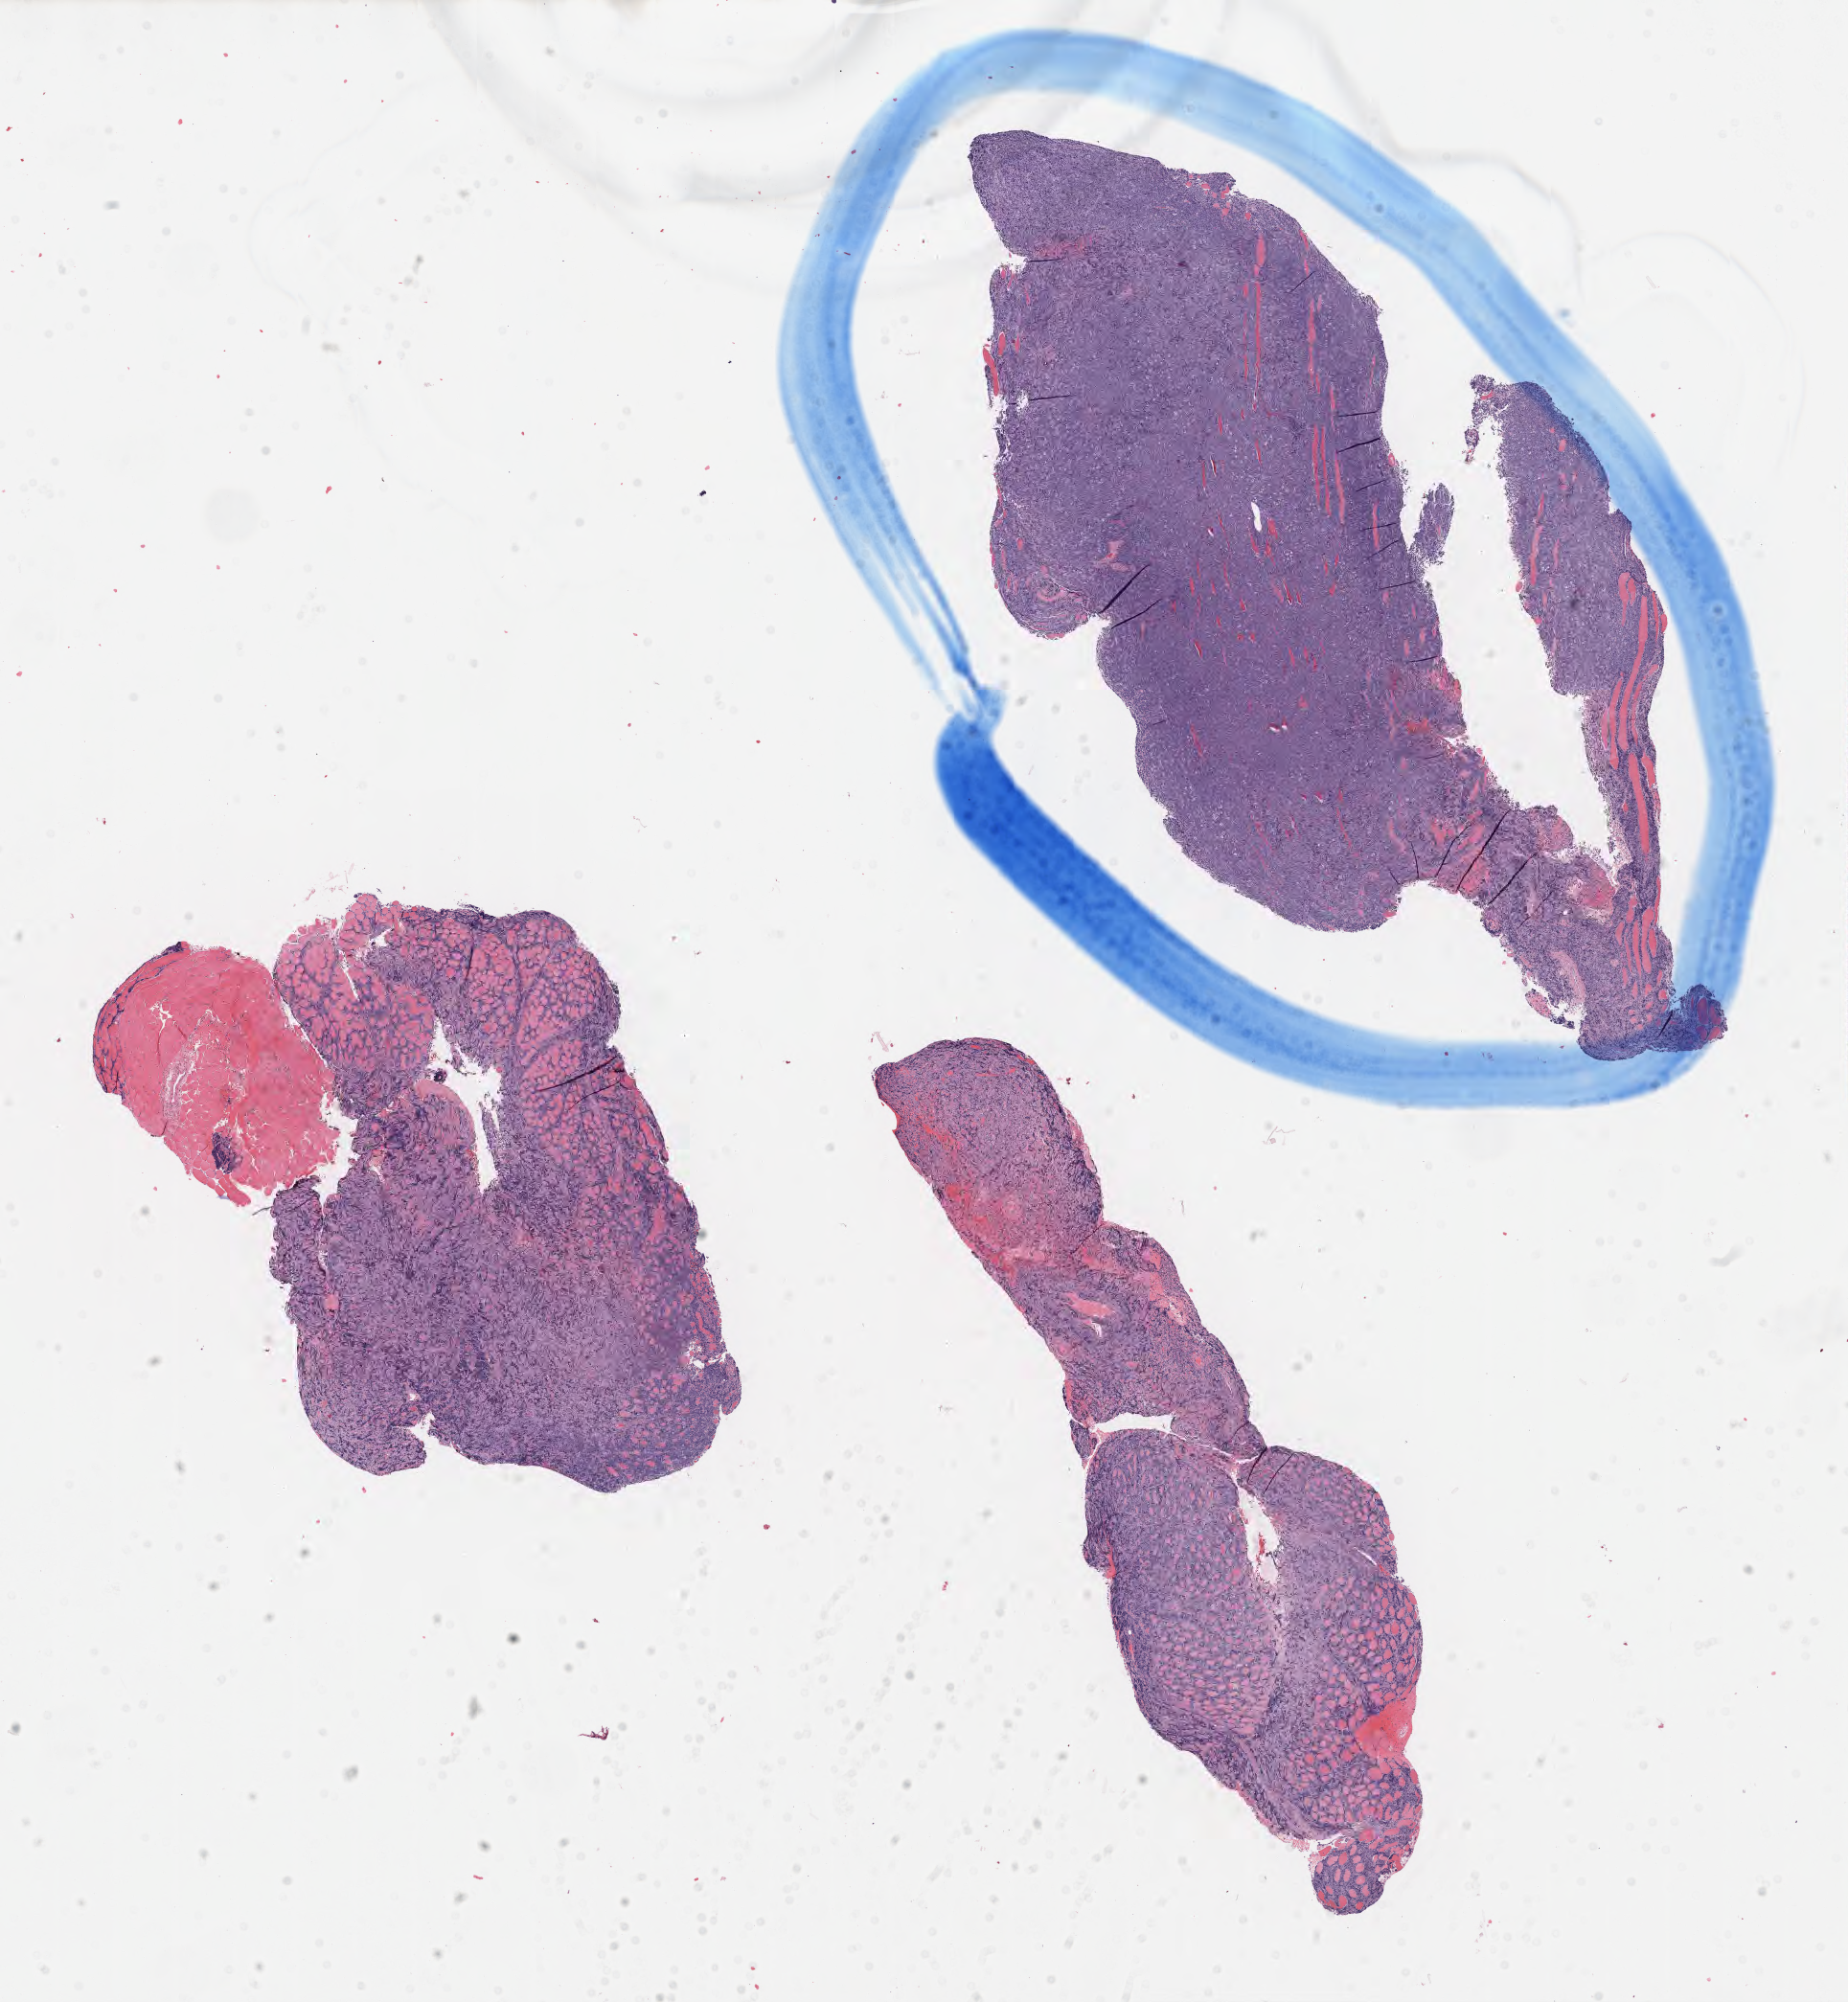
H&E whole-slide image — whole scanned area (about 15.6 x 16.9 mm) shown as a low-resolution overview; specimen: tumor tissue; anatomic site: lymph node of head and neck. Male patient, age 55 years.
* diagnosis: Burkitt lymphoma, NOS